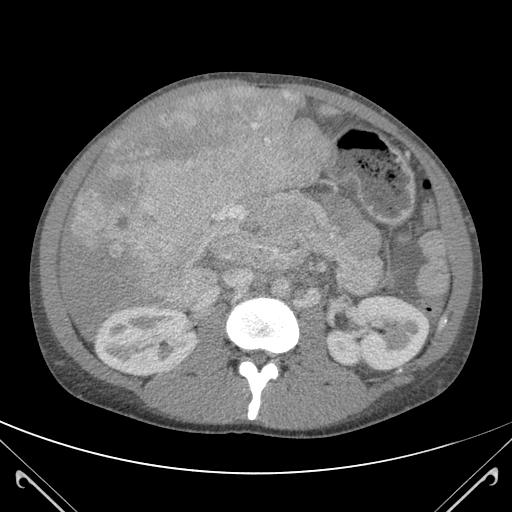
Contrast-enhanced abdominal CT (liver protocol), one axial slice; slice 58 of 118 in the series (ordered by position); soft-tissue window (W 400 / L 40 HU); 3 mm slice thickness; 512 × 512 image matrix, field of view 380 × 380 mm. Case-level facts recorded for this patient, not image findings: diagnosis: hepatocellular carcinoma (patient treated with transarterial chemoembolisation; whether this scan precedes or follows treatment is not stated here); TNM stage (as recorded): Stage-IIIB; Child-Pugh class: A; tumour nodularity: uninodular.
Structures marked on this image (semi-automatic segmentation, software-assisted and operator-edited):
- abdominal aorta: bounding box [x1, y1, x2, y2] px = [272, 279, 290, 299]
- liver parenchyma outside the tumour (the mass and vessels are separate outlines, so this box may not span the whole liver): [59, 87, 330, 334]
- mass: [72, 89, 326, 313]
- liver vessels: [190, 89, 315, 303]